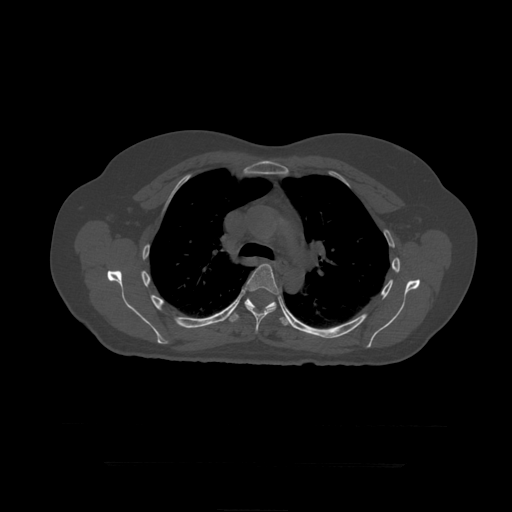
CT including the spine, one axial slice; slice 314 of 399 in the series (ordered by position); bone window (W 1800 / L 400 HU); 1.25 mm slice thickness; 512 × 512 image matrix, field of view 450 × 450 mm. Patient age 41 years. Case-level facts recorded for this patient, not image findings: primary cancer: breast.
Annotated regions visible in this slice (semi-automatic segmentation, software-assisted and operator-edited):
- T6 vertebra: bounding box (x1, y1, x2, y2) in pixels: (229, 264, 279, 334)
- T7 vertebra: (229, 298, 290, 326)